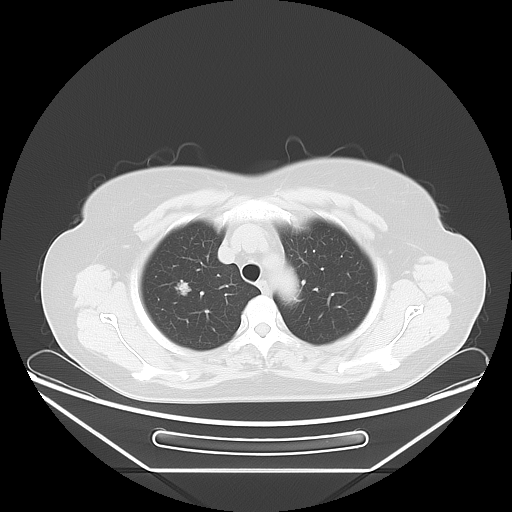
Chest CT, one axial slice; position 49 of 59 along the scan axis; reconstruction kernel LUNG; lung window (W 1500 / L -600 HU); 5 mm slice thickness; 512 × 512 image matrix. Patient: female, 60 years. From the clinical record (not read from this slice): clinical TNM (as recorded): T1c N0 M0.
Outlined on this slice (rectangle marked by the reading radiologist):
- lung tumour (recorded histology: adenocarcinoma): bounding box [x1, y1, x2, y2] px = [168, 274, 197, 303]